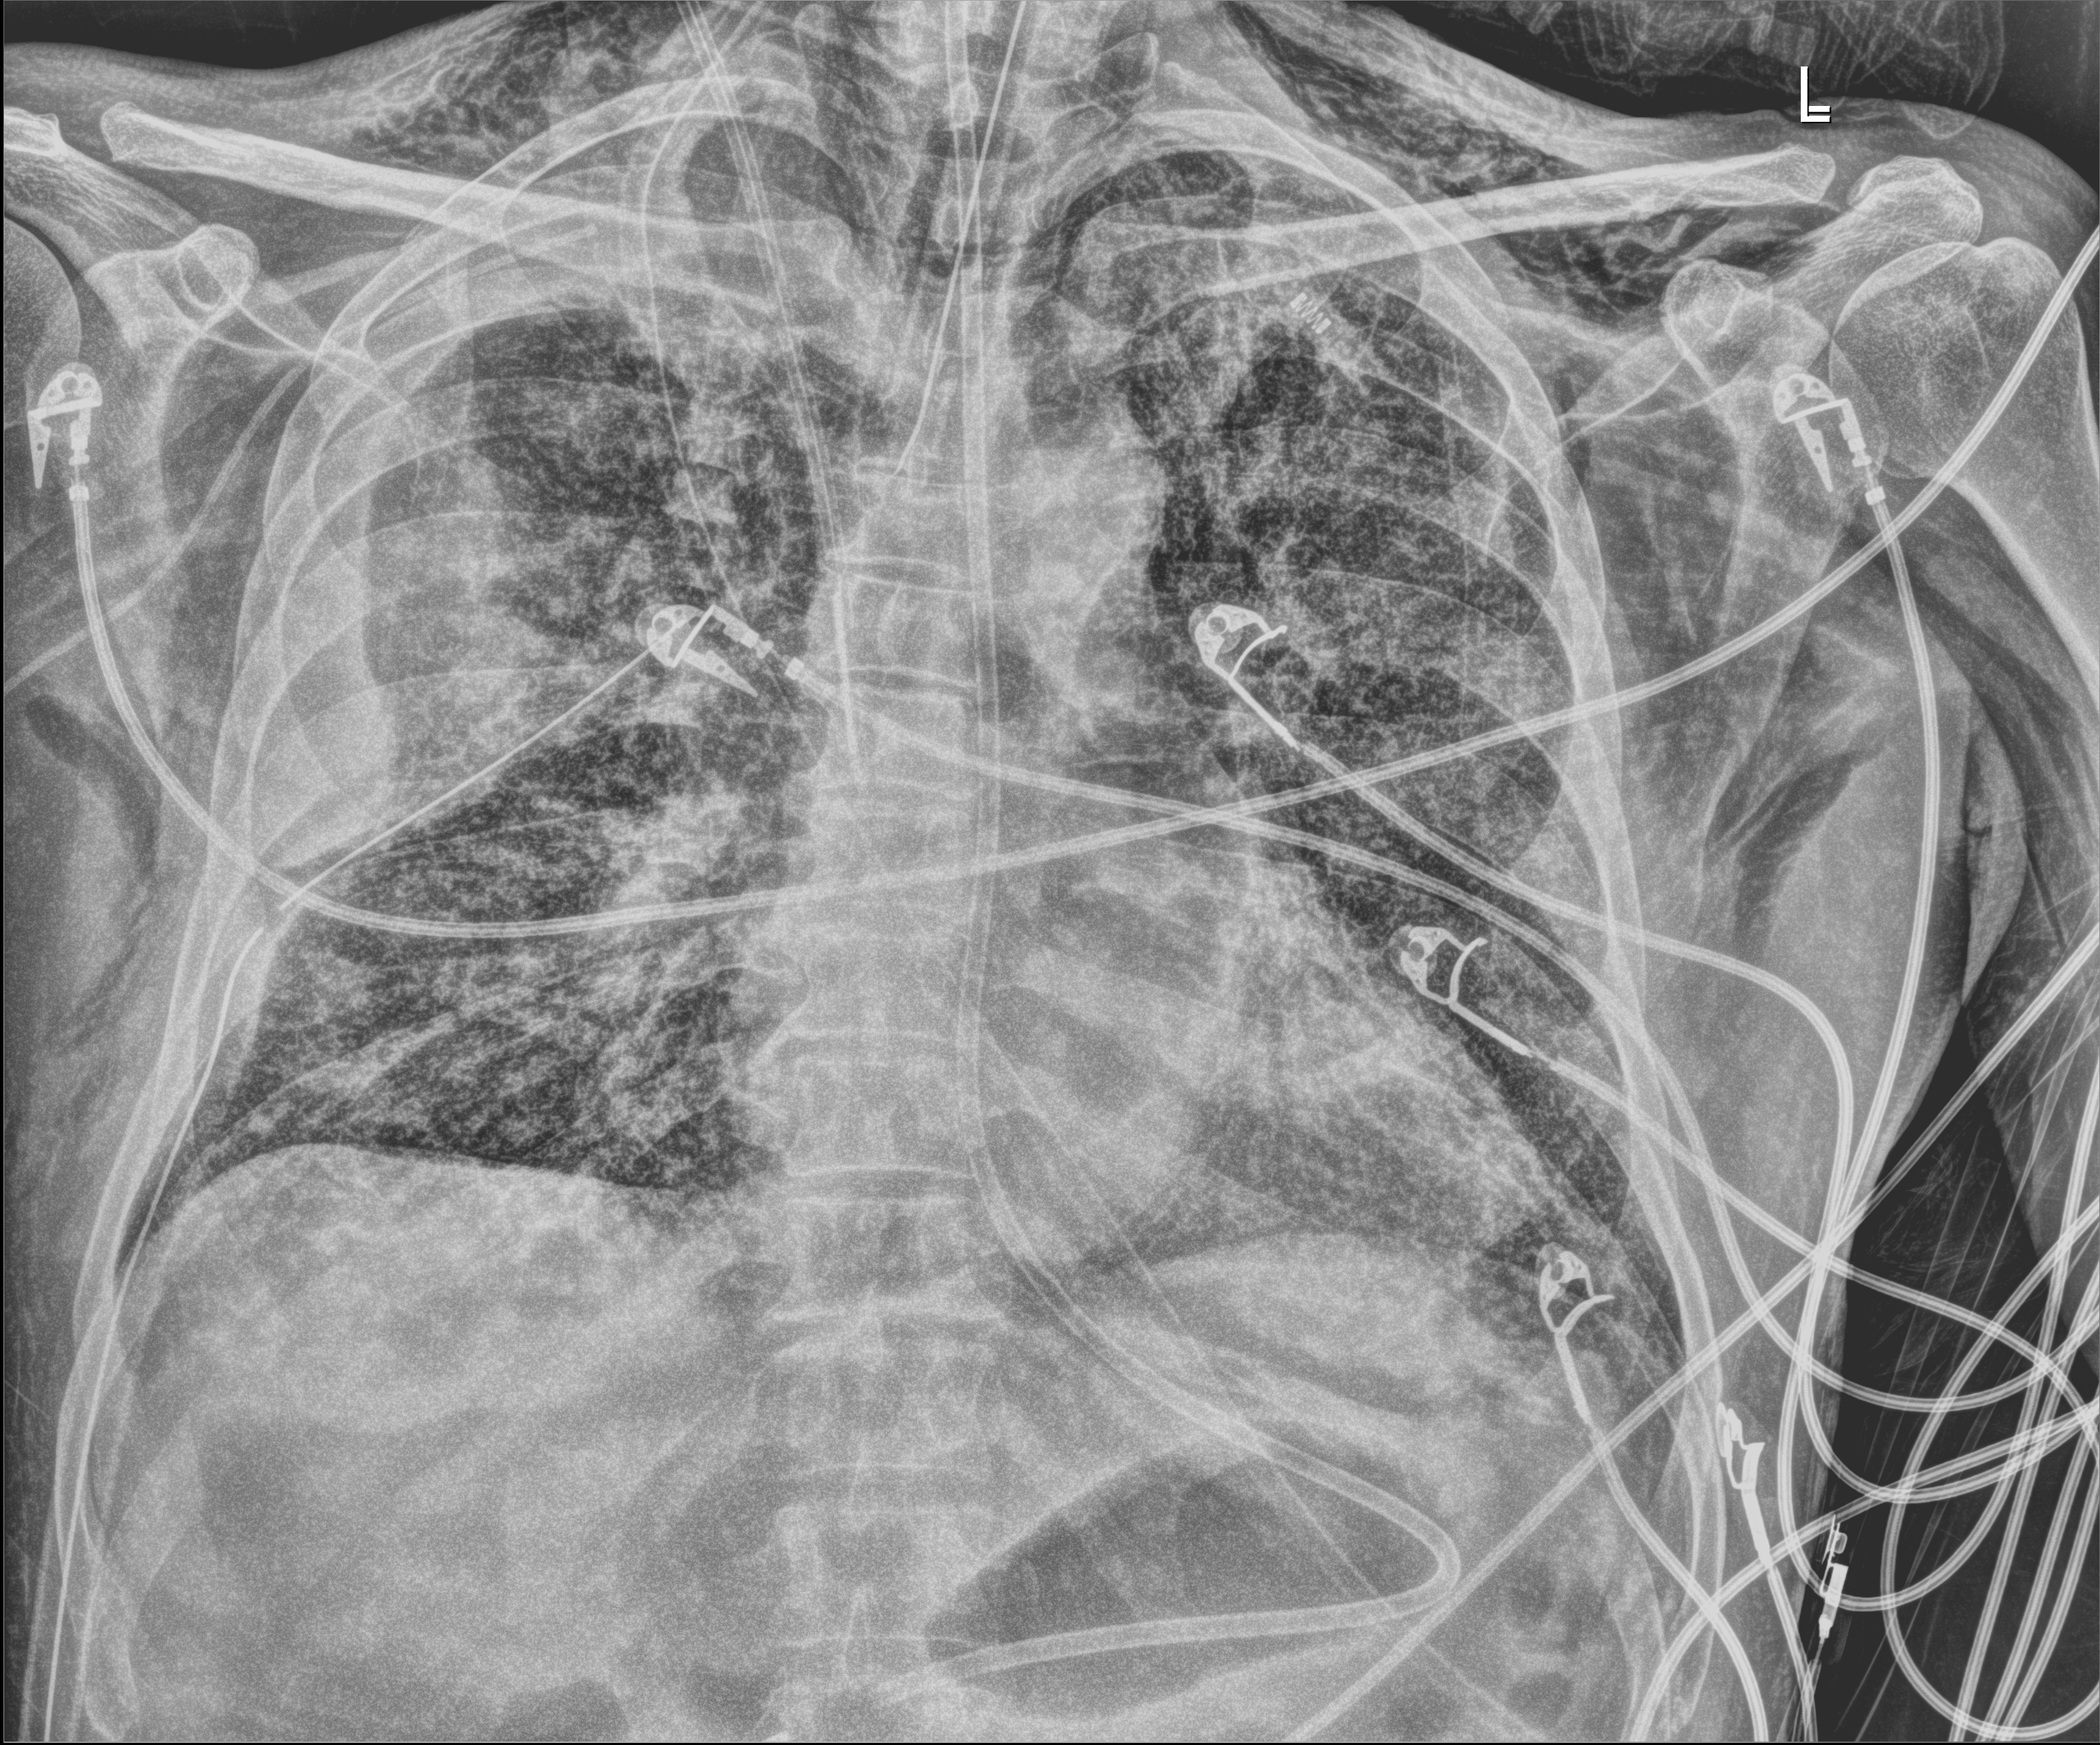
Chest X-ray (portable), anteroposterior (AP) projection. Male patient hospitalised with COVID-19, age 18–59 years.
Admission-level facts for this patient (not findings on this image; timing relative to this image not recorded):
- mechanically ventilated during this hospital stay: yes